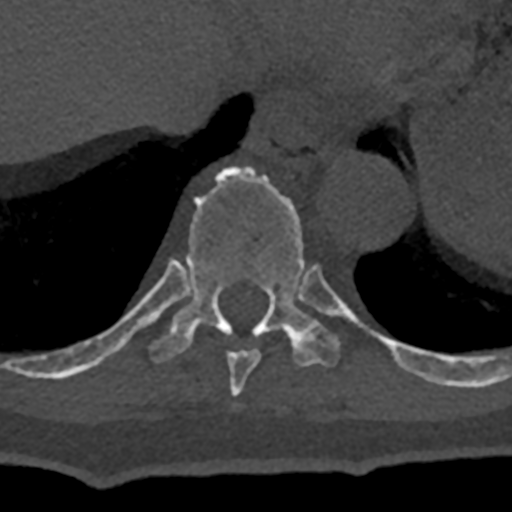
CT including the spine, one axial slice. Slice 619 of 797 in the series (ordered by position). Reconstruction kernel Br40s/3. 120 kVp. Bone window (W 1800 / L 400 HU). 512 × 512 image matrix. Male patient, age 74 years. From the clinical record (not read from this slice): primary cancer: renal; vertebrae with lytic lesions (as recorded): T10, L1, L2, L3, L4, L5.
Structures marked on this image (semi-automatically segmented with operator editing):
- T10 vertebra: bounding box (x1, y1, x2, y2) in pixels: (70, 166, 432, 382)
- T9 vertebra: (227, 348, 261, 397)